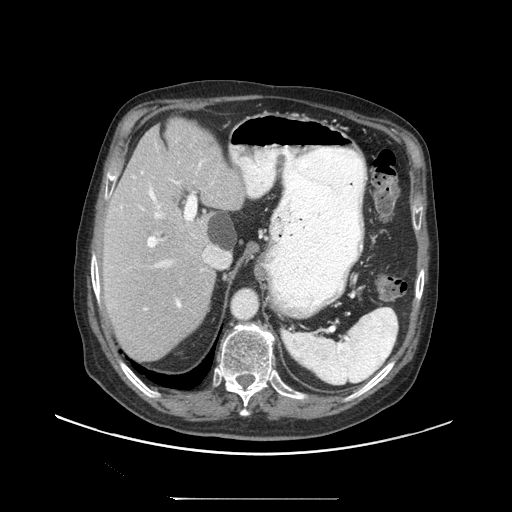
Contrast-enhanced abdominal CT (liver protocol), one axial slice. Slice 68 of 97 in the series (ordered by position). Reconstruction kernel STANDARD. 140 kVp. Soft-tissue window (W 400 / L 40 HU). 2.5 mm slice thickness. 512 × 512 image matrix. Case-level facts recorded for this patient, not image findings: diagnosis: hepatocellular carcinoma (patient treated with transarterial chemoembolisation; whether this scan precedes or follows treatment is not stated here); TNM stage (as recorded): Stage-IIIC; Child-Pugh class: A; tumour nodularity: uninodular; tumour size: 9.2 cm.
Outlined on this slice (semi-automatic segmentation, software-assisted and operator-edited):
- abdominal aorta: bounding box (x1, y1, x2, y2) in pixels: (233, 290, 256, 318)
- liver parenchyma outside the tumour (the mass and vessels are separate outlines, so this box may not span the whole liver): (102, 118, 244, 360)
- liver vessels: (133, 161, 202, 308)